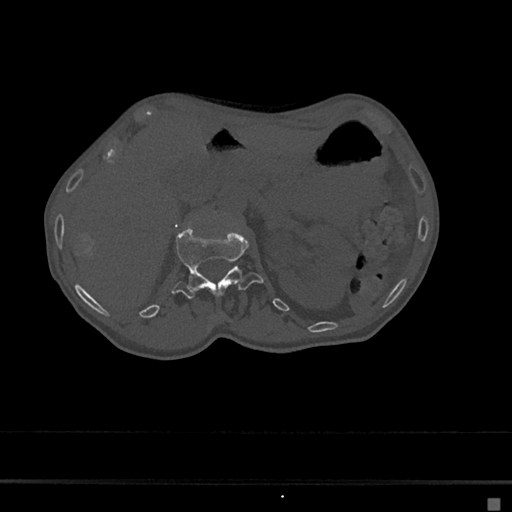
CT including the spine, one axial slice; position 71 of 797 along the scan axis; reconstruction kernel Br40s/3; 120 kVp; bone window (W 1800 / L 400 HU); 0.5 mm slice thickness; 512 × 512 image matrix, field of view 360 × 360 mm. Female patient, age 68 years. From the clinical record (not read from this slice): primary cancer: renal.
Structures marked on this image (semi-automatically segmented with operator editing):
- L1 vertebra: bounding box <172,223,264,299> (left, top, right, bottom; pixels)